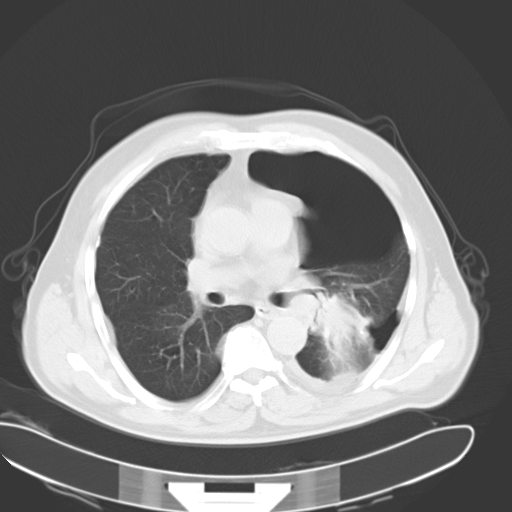
Chest CT, one axial slice. Position 20 of 34 along the scan axis. Reconstruction kernel B40f. Lung window (W 1500 / L -600 HU). 512 × 512 image matrix. Male patient, age 62 years. Case-level facts recorded for this patient, not image findings: clinical TNM (as recorded): T3 N0 M1.
Outlined on this slice (rectangle marked by the reading radiologist):
- lung tumour (recorded histology: adenocarcinoma): box from (x=316, y=294) to (x=377, y=362) px
- lung tumour (recorded histology: adenocarcinoma): (x=317, y=288)–(x=371, y=355)